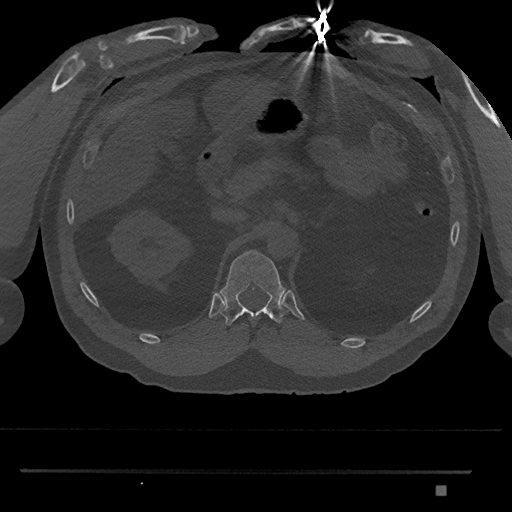
CT including the spine, one axial slice; slice 893 of 1134 in the series (ordered by position); 120 kVp; bone window (W 1800 / L 400 HU); 0.5 mm slice thickness; 512 × 512 image matrix. Male patient, age 65 years. From the clinical record (not read from this slice): primary cancer: prostate.
Outlined on this slice (semi-automatic segmentation, software-assisted and operator-edited):
- T12 vertebra: bounding box <219,250,288,325> (left, top, right, bottom; pixels)